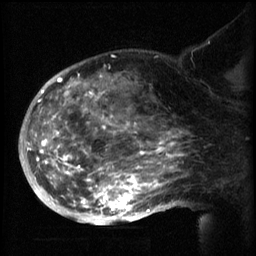
Breast MRI (dynamic contrast-enhanced), one sagittal slice; slice 39 of 60 in the series (ordered by position); 3 images stored at this slice position (order not interpretable as contrast timing); 1.5 T; TE 4.2 ms, TR 8.2 ms; 2.3 mm slice thickness; 256 × 256 image matrix, field of view 200 × 200 mm. Female patient, age 50 years.
Outlined on this slice (semi-automatic segmentation, software-assisted and operator-edited):
- analysis volume of interest (the breast-tissue region the enhancement analysis was run in; not a lesion): bounding box <50,64,169,217> (left, top, right, bottom; pixels)
- tumour enhancement mask (voxels above the 70 % enhancement threshold inside the analysis volume of interest): <50,70,169,215>